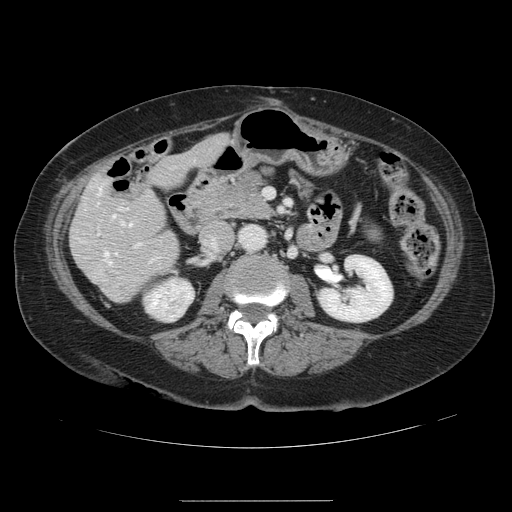
Contrast-enhanced abdominal CT, one axial slice. 120 kVp. Soft-tissue window (W 400 / L 40 HU). 512 × 512 image matrix. Female patient, age 74 years. Case-level facts recorded for this patient, not image findings: diagnosis: colorectal cancer liver metastases, imaged before liver resection; multiple liver metastases: yes; largest metastasis: 7 cm; disease in both lobes: yes.
Annotated regions visible in this slice (outlined manually by an expert reader):
- hepatic veins: bounding box [x1, y1, x2, y2] px = [98, 188, 132, 263]
- liver: [71, 135, 228, 303]
- planned liver remnant (the part of the liver to remain after resection): [72, 135, 228, 303]
- portal vein (with intrahepatic branches): [98, 207, 140, 247]